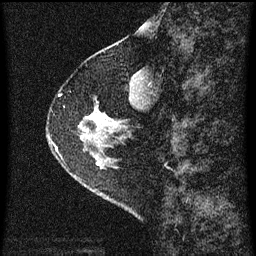
Breast MRI (dynamic contrast-enhanced), one sagittal slice. Slice 21 of 60 in the series (ordered by position). Dynamic contrast-enhanced series, image 2 of 3 at this slice position (ordered by acquisition). 1.5 T. TE 4.2 ms, TR 8 ms. 2 mm slice thickness. 256 × 256 image matrix, field of view 180 × 180 mm. Female patient, age 56 years.
Annotated regions visible in this slice (semi-automatic segmentation, software-assisted and operator-edited):
- analysis volume of interest (the breast-tissue region the enhancement analysis was run in; not a lesion): bounding box <49,108,110,159> (left, top, right, bottom; pixels)
- tumour enhancement mask (voxels above the 70 % enhancement threshold inside the analysis volume of interest): <90,112,108,123>